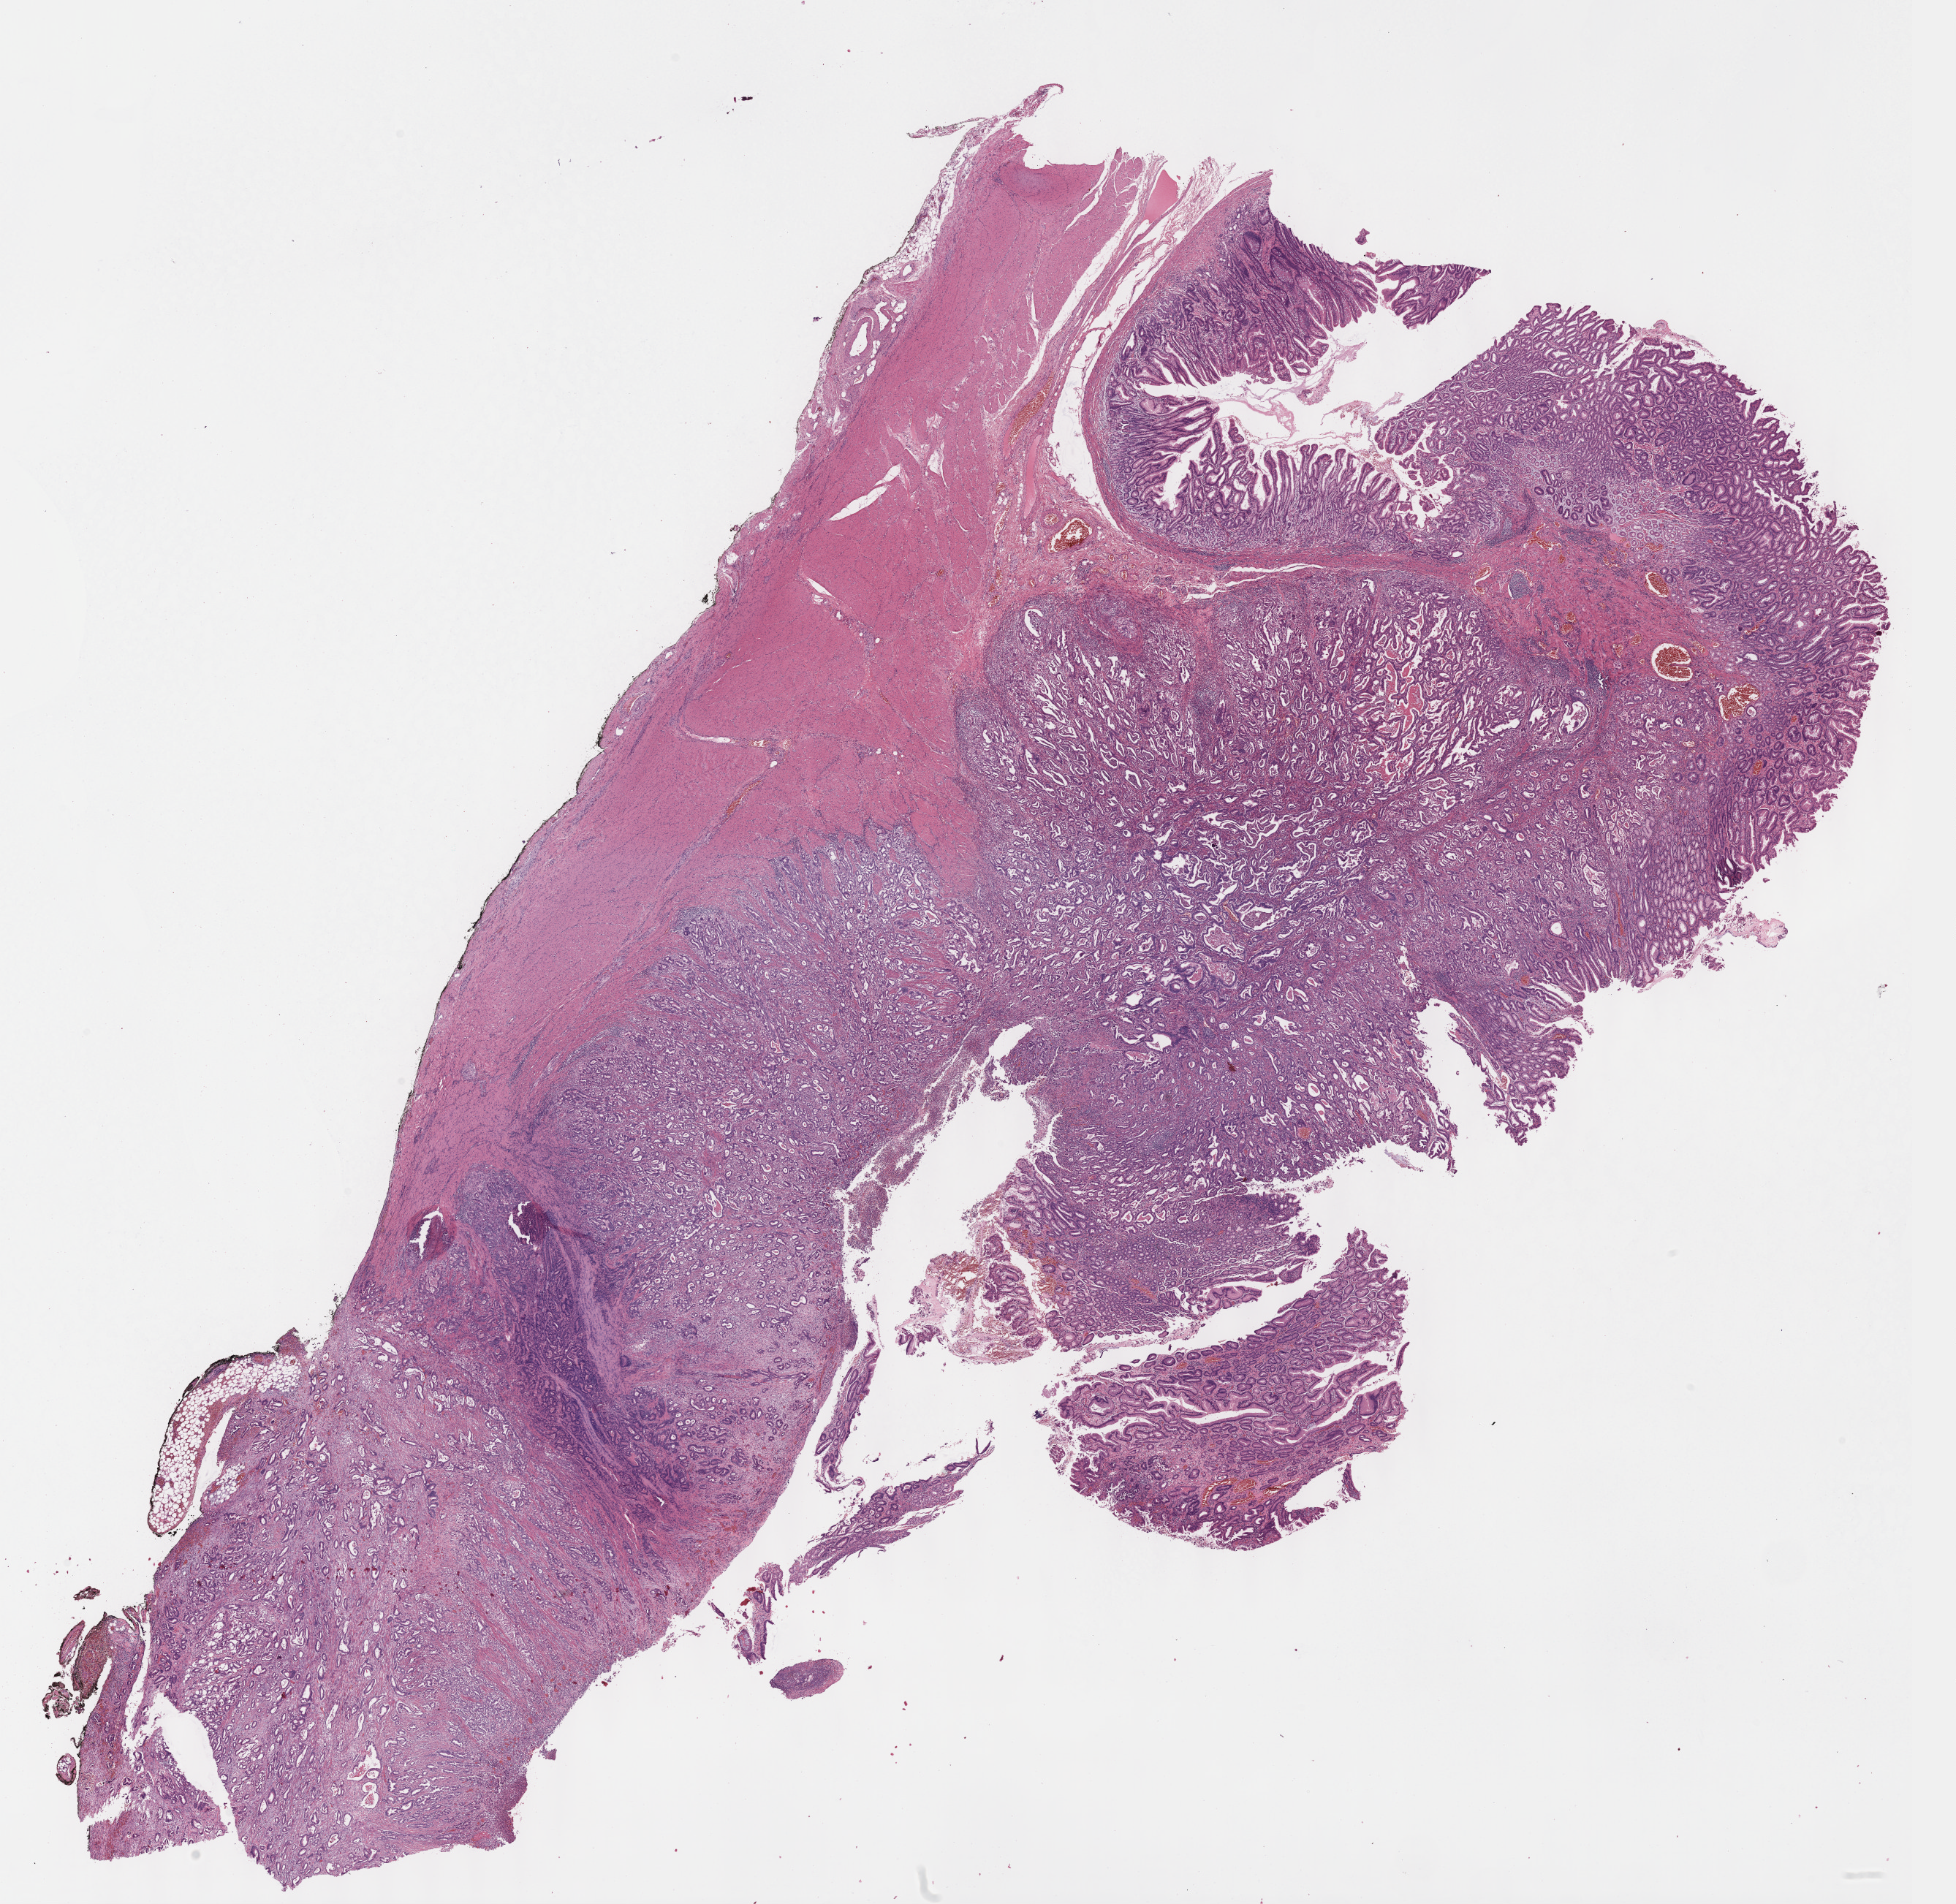
Hematoxylin and eosin (H&E) stained whole-slide image — low-resolution overview of the scanned area, about 21.6 x 21.1 mm. FFPE section. Primary tumour sample from the stomach. Patient: male, age at initial diagnosis 69 years. Histologic grade: G2 (moderately differentiated).
AJCC pathologic stage: IIIA (6th edition). Lymph nodes positive (case pathology): 4 of 31 examined. Diagnosis: Adenocarcinoma, intestinal type (gastric antrum).